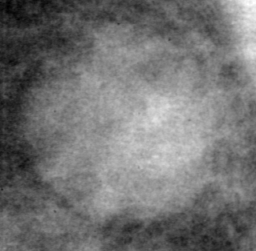
Region of interest cut from a scanned film mammogram (one marked finding), left breast, MLO view, BI-RADS breast density category 3 (scale 1–4).
Marked abnormality: mass, shape round, margins circumscribed; BI-RADS assessment category 3; pathology result (as recorded, not read from the image): benign.